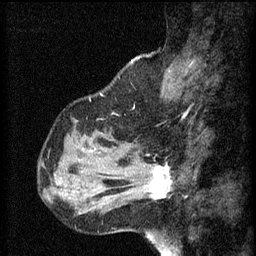
Breast MRI (dynamic contrast-enhanced), one sagittal slice. Slice 17 of 60 in the series (ordered by position). 3 images stored at this slice position (order not interpretable as contrast timing). 1.5 T. TE 4.2 ms, TR 8.2 ms. 2 mm slice thickness. 256 × 256 image matrix. Patient: female, 37 years.
Structures marked on this image (semi-automatically segmented with operator editing):
- analysis volume of interest (the breast-tissue region the enhancement analysis was run in; not a lesion): bounding box [x1, y1, x2, y2] px = [126, 156, 172, 205]
- tumour enhancement mask (voxels above the 70 % enhancement threshold inside the analysis volume of interest): [147, 166, 171, 199]